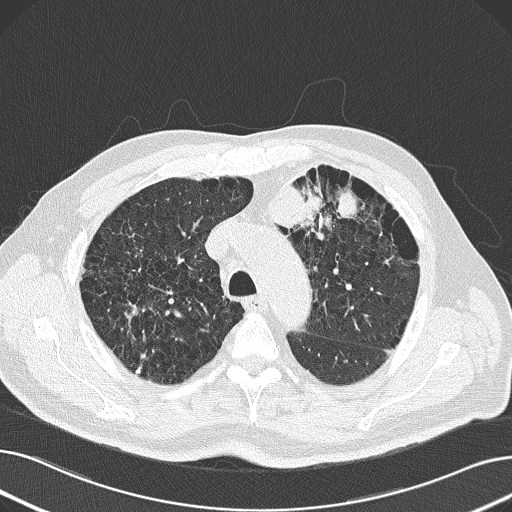
Chest CT (low-dose screening protocol), one axial image. Baseline screening round. Lung window (W 1500 / L -600 HU). 2 mm slice thickness. 120 kVp. Slice 52 of 165 in the series. 512 × 512 image matrix, field of view 370 × 370 mm. Male, age 69 years at enrolment.
Expert reader's lesion annotation, bounding box <225,150,379,255> (left, top, right, bottom; pixels). The exam's reader record, not a measurement of the box and not confirmed to be the same lesion: non-calcified nodule or mass ≥4 mm, left upper lobe, 6 × 10 mm, spiculated (stellate) margins, soft tissue attenuation. Official screen result: positive, change unspecified: nodule(s) >= 4 mm or enlarging nodule(s), mass(es), or other non-specific abnormalities suspicious for lung cancer. Later outcome: lung cancer diagnosed 20 days after this screen — non-small cell carcinoma, left upper lobe, poorly differentiated (G3), stage IB (AJCC 6th edition), 100 mm at pathology.